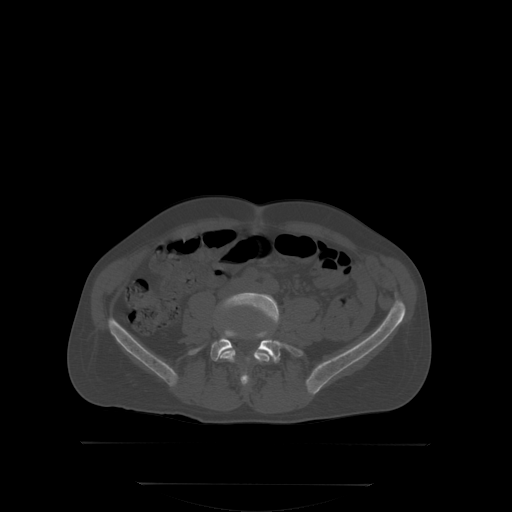
CT including the spine, one axial slice. Slice 101 of 350 in the series (ordered by position). Bone window (W 1800 / L 400 HU). 2.5 mm slice thickness. 512 × 512 image matrix, field of view 500 × 500 mm. Male patient, age 58 years. From the clinical record (not read from this slice): primary cancer: prostate.
Structures marked on this image (semi-automatic segmentation, software-assisted and operator-edited):
- L4 vertebra: bounding box <218,293,278,386> (left, top, right, bottom; pixels)
- L5 vertebra: <188,328,301,362>